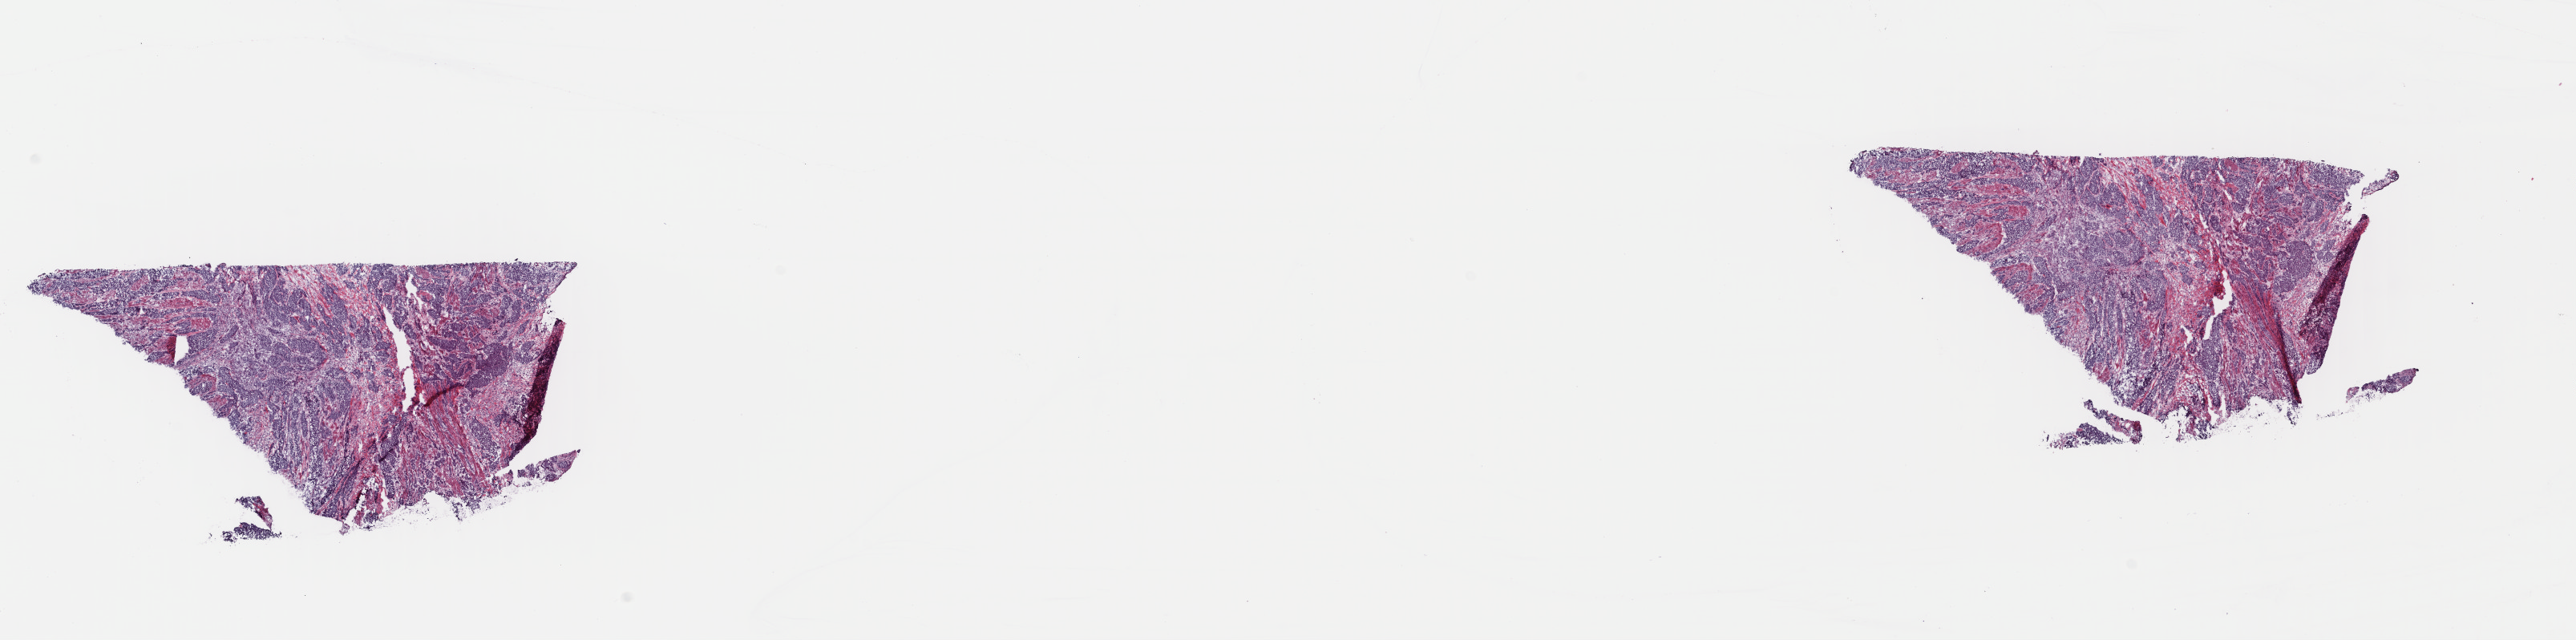
Digitized Hematoxylin and eosin (H&E) stained tissue section (whole slide), a low-resolution overview of the entire scanned area, about 25.3 x 6.3 mm (slide scanned at 40x). Frozen section from the top of the tissue portion. Sample: primary tumour, bladder. Patient: female, age at initial diagnosis 67 years. Histologic grade: high grade. Composition of this section per pathologist review: tumour cells 50%, tumour nuclei 75%, normal cells 0%, stromal cells 49%, necrosis 1%. Inflammatory infiltration, as recorded: lymphocyte infiltration 5%, monocyte infiltration 0%, neutrophil infiltration 0%.
Lymph nodes positive (case pathology): 0 of 5 examined. Diagnosis: Transitional cell carcinoma (posterior wall of bladder). AJCC pathologic stage: III (7th edition).